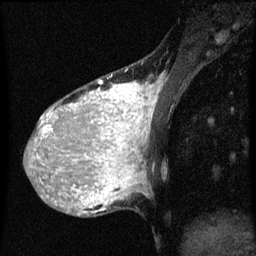
Breast MRI (dynamic contrast-enhanced), one sagittal slice; slice 16 of 60 in the series (ordered by position); dynamic contrast-enhanced series, image 2 of 3 at this slice position (ordered by acquisition); 1.5 T; TE 4.2 ms, TR 8 ms; 256 × 256 image matrix, field of view 180 × 180 mm. Patient: female, 36 years.
Annotated regions visible in this slice (semi-automatically segmented with operator editing):
- analysis volume of interest (the breast-tissue region the enhancement analysis was run in; not a lesion): bounding box (x1, y1, x2, y2) in pixels: (32, 68, 161, 161)
- tumour enhancement mask (voxels above the 70 % enhancement threshold inside the analysis volume of interest): (34, 80, 157, 161)